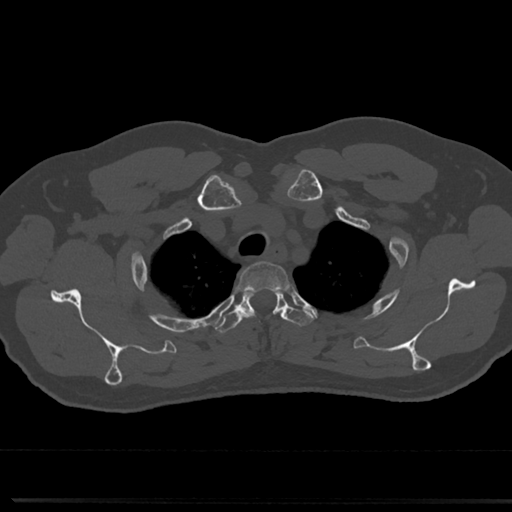
CT including the spine, one axial slice; slice 609 of 817 in the series (ordered by position); bone window (W 1800 / L 400 HU); 0.5 mm slice thickness; 512 × 512 image matrix, field of view 355 × 355 mm. Patient: male, 61 years. From the clinical record (not read from this slice): primary cancer: prostate.
Structures marked on this image (semi-automatic segmentation, software-assisted and operator-edited):
- T2 vertebra: bounding box [x1, y1, x2, y2] px = [239, 262, 289, 285]
- T3 vertebra: [215, 287, 308, 333]